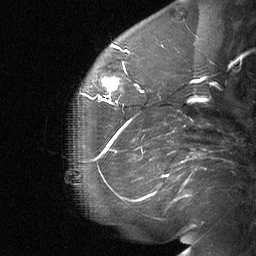
Breast MRI (dynamic contrast-enhanced), one sagittal slice. Position 20 of 64 along the scan axis. Dynamic contrast-enhanced study with each time point stored as its own series, time point 2 of 3 at this slice position (early post-contrast, ordered by acquisition time). 1.5 T. TE 4.8 ms, TR 27 ms. 2 mm slice thickness. 256 × 256 image matrix, field of view 200 × 200 mm. Patient: female, 60 years. Case-level facts recorded for this patient, not image findings: setting: breast cancer imaged before/during neoadjuvant chemotherapy; receptor status: HR-positive, HER2-negative.
Outlined on this slice (semi-automatically segmented with operator editing):
- analysis volume of interest (the breast-tissue region the enhancement analysis was run in; not a lesion): bounding box <91,56,139,104> (left, top, right, bottom; pixels)
- tumour enhancement mask (voxels above the 90 % enhancement threshold inside the analysis volume of interest): <97,77,138,103>